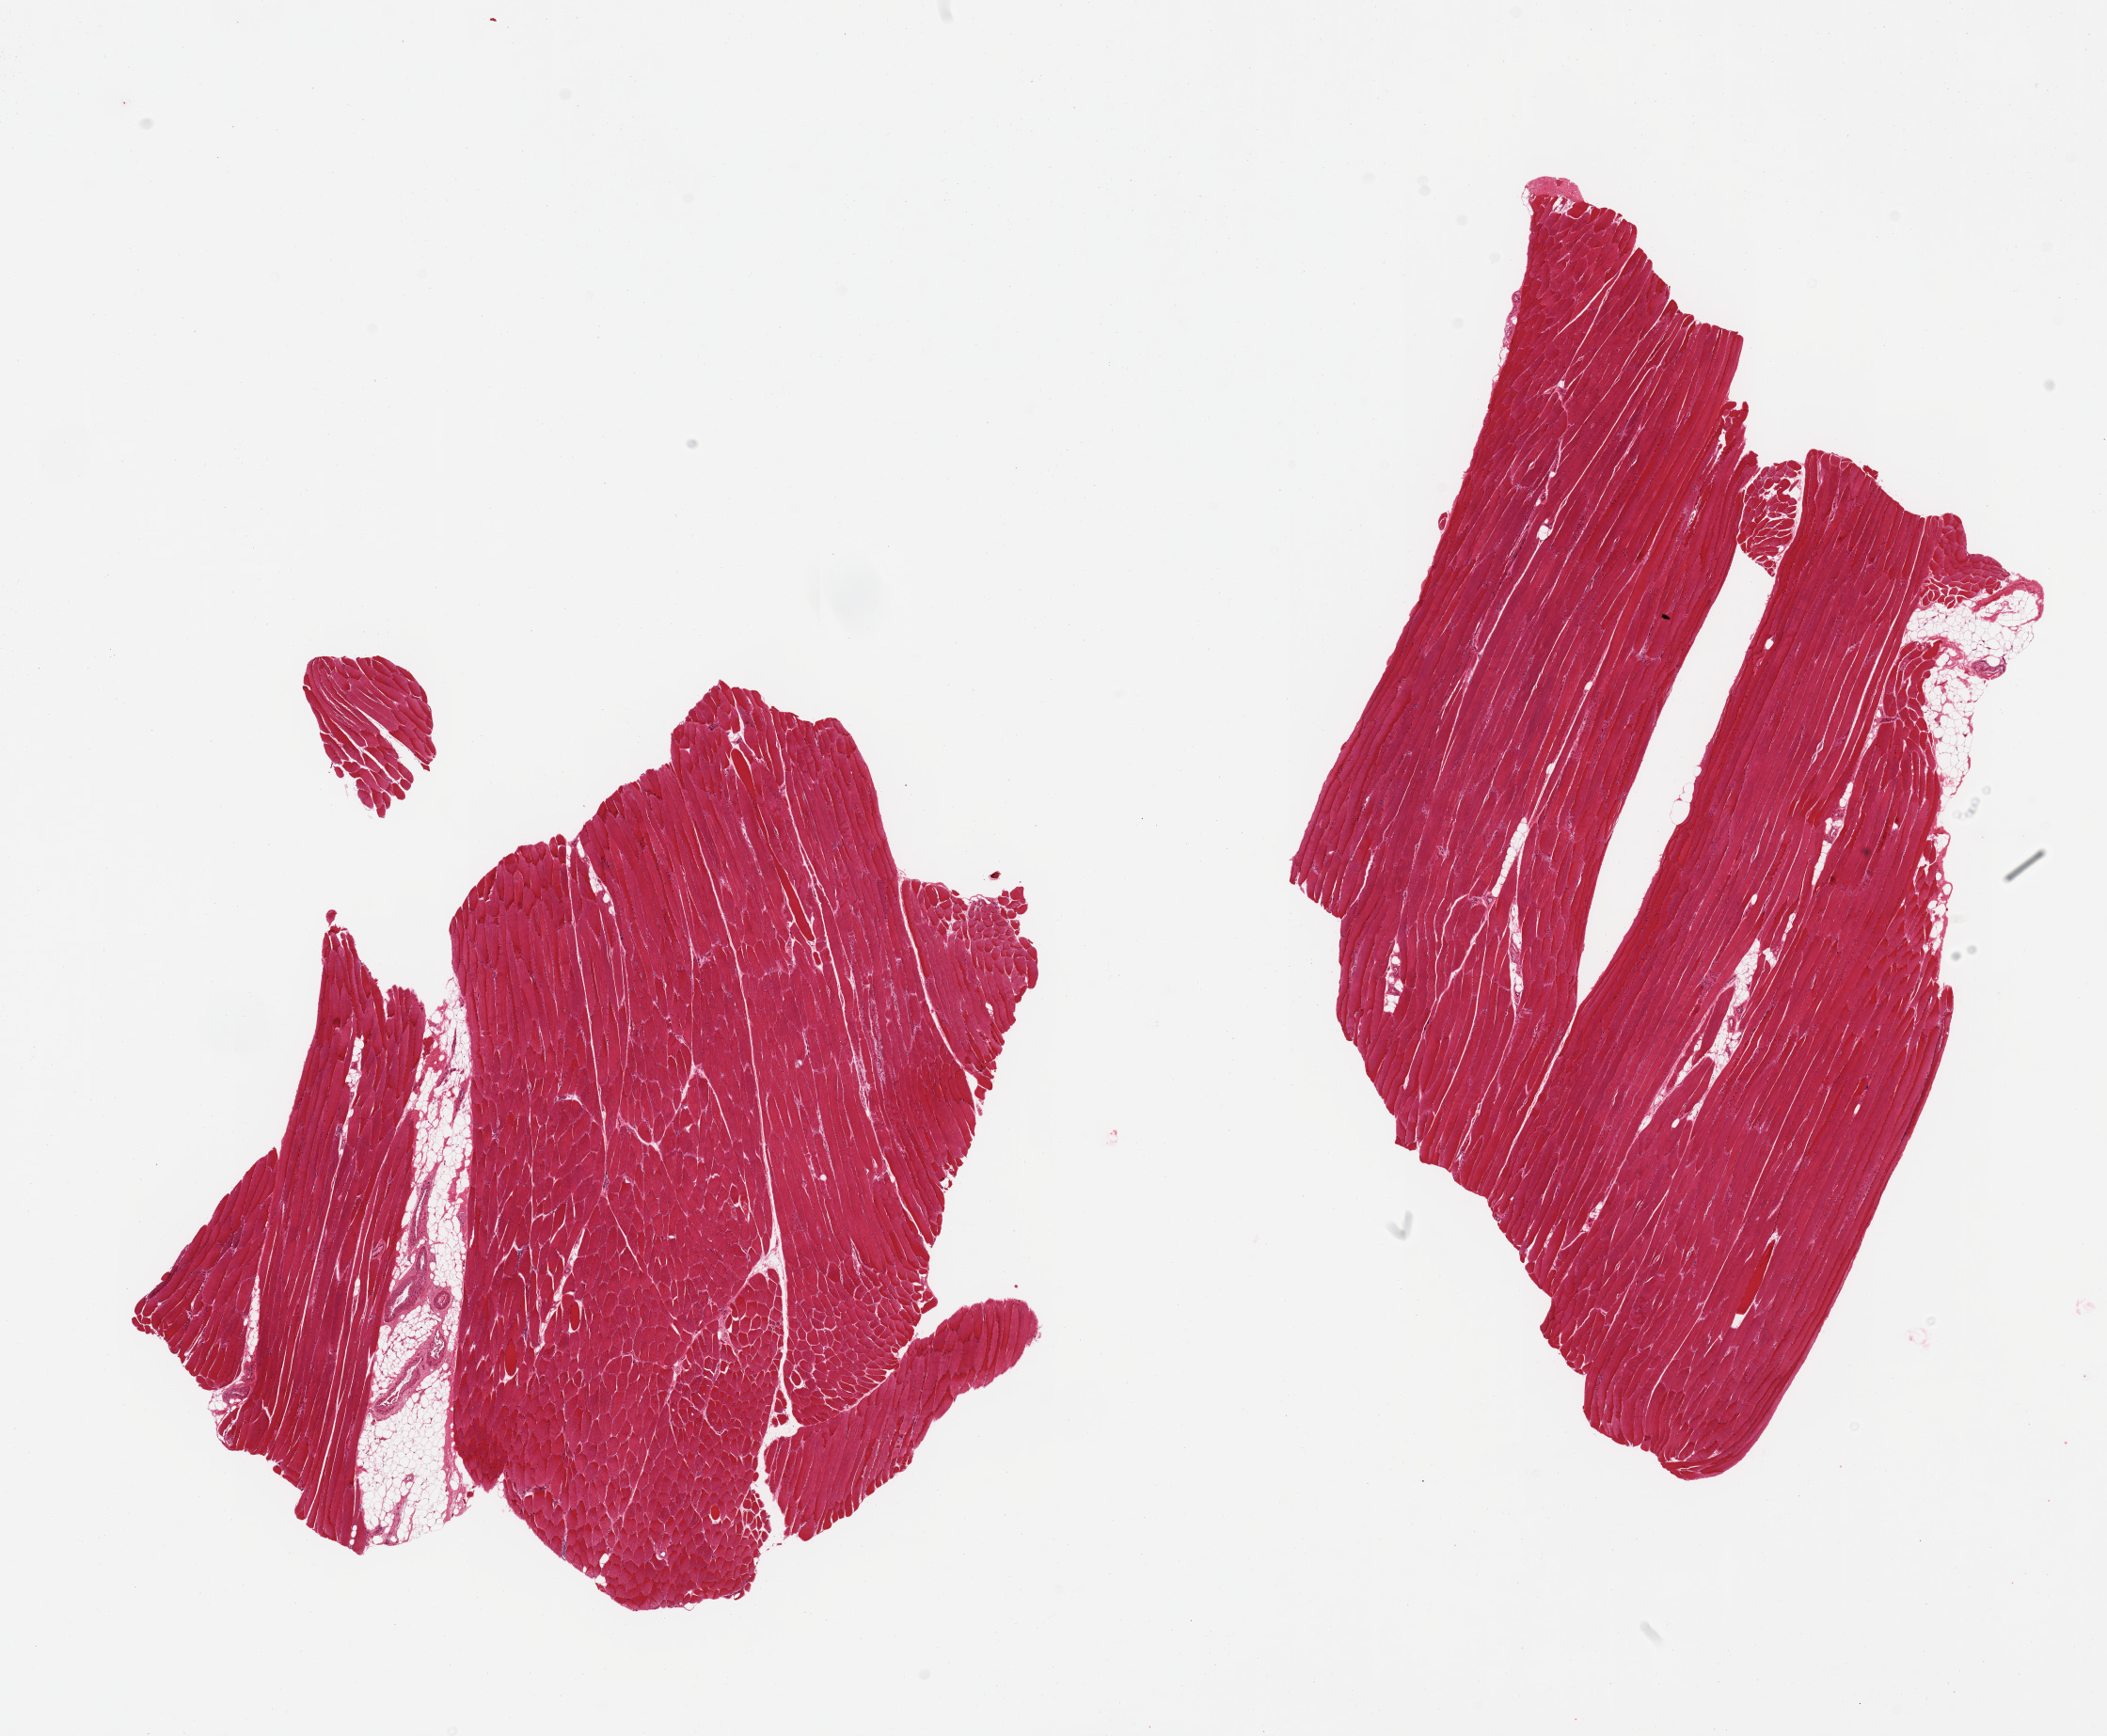
Whole-slide image, haematoxylin and eosin stain — shown as a low-resolution overview of the whole scanned area (about 17.7 x 14.6 mm). PAXgene-fixed paraffin-embedded (PFPE) section. Sampled site (target tissue): skeletal muscle. Donor tissue sample.
Review note (as recorded): 6 pieces, Minimal interstitial fat, ~10%.